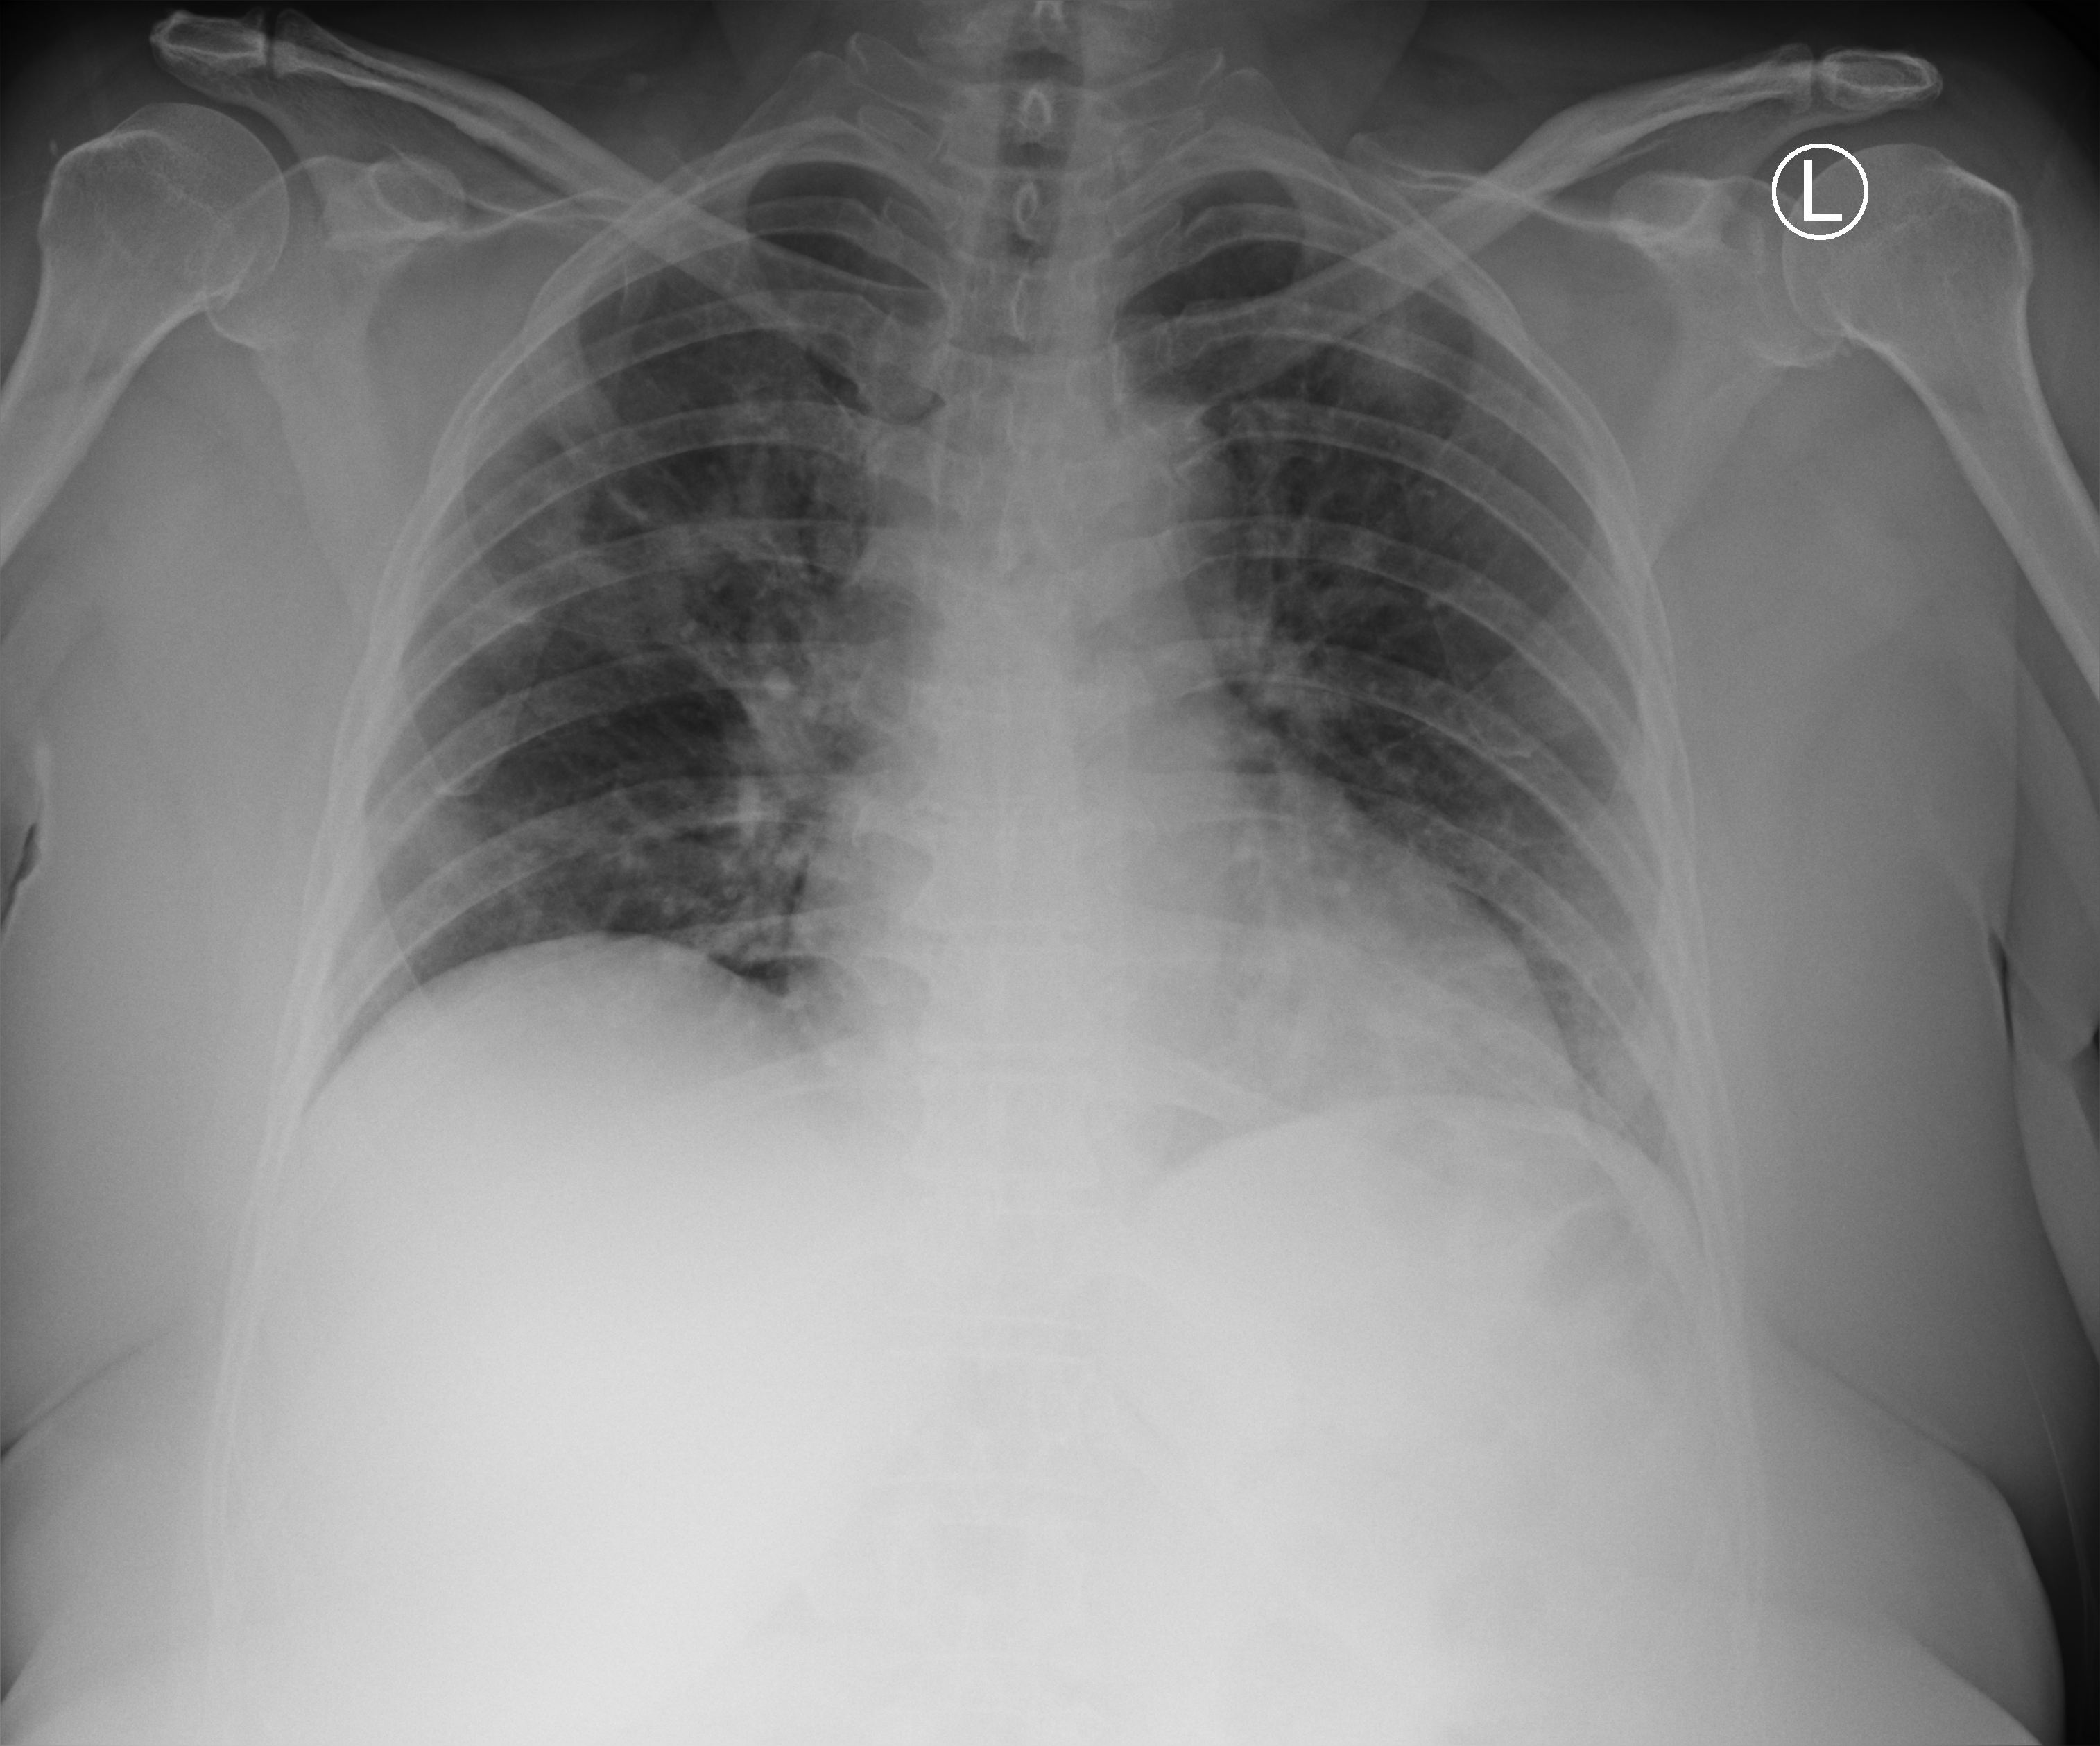
Chest X-ray (portable), anteroposterior (AP) projection. Female patient hospitalised with COVID-19, age 60–74 years.
Admission-level facts for this patient (not findings on this image; timing relative to this image not recorded): length of hospital stay: 1 day; admitted to intensive care during this hospital stay: no.